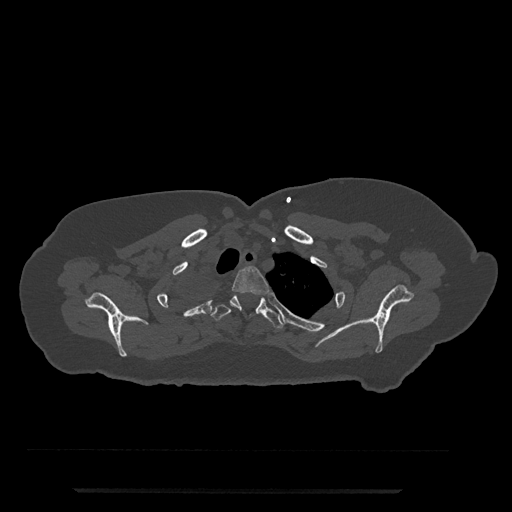
CT including the spine, one axial slice. Slice 652 of 797 in the series (ordered by position). Reconstruction kernel Br40s/3. Bone window (W 1800 / L 400 HU). 512 × 512 image matrix, field of view 440 × 440 mm. Patient: female, 51 years. From the clinical record (not read from this slice): primary cancer: neuro; vertebrae with lytic lesions (as recorded): T8.
Outlined on this slice (semi-automatically segmented with operator editing):
- T2 vertebra: bounding box <231,266,269,295> (left, top, right, bottom; pixels)
- T3 vertebra: <191,295,284,329>